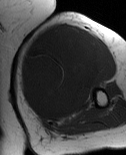
MRI of an extremity soft-tissue mass, one axial slice; position 43 of 86 along the scan axis; MR volume resampled by the dataset authors to the PET/CT grid (not the native acquisition matrix); 3.27 mm slice thickness; 126 × 155 image matrix, field of view 123 × 151 mm. Female patient. Case-level facts recorded for this patient, not image findings: histological type: pleiomorphic leiomyosarcoma; grade: high; site of the primary tumour: left biceps.
Structures marked on this image (expert contour drawn on MRI and transferred to this co-registered scan by the dataset authors):
- gross tumour volume including surrounding oedema: bounding box <20,26,108,121> (left, top, right, bottom; pixels)
- gross tumour volume (mass): <20,26,105,119>